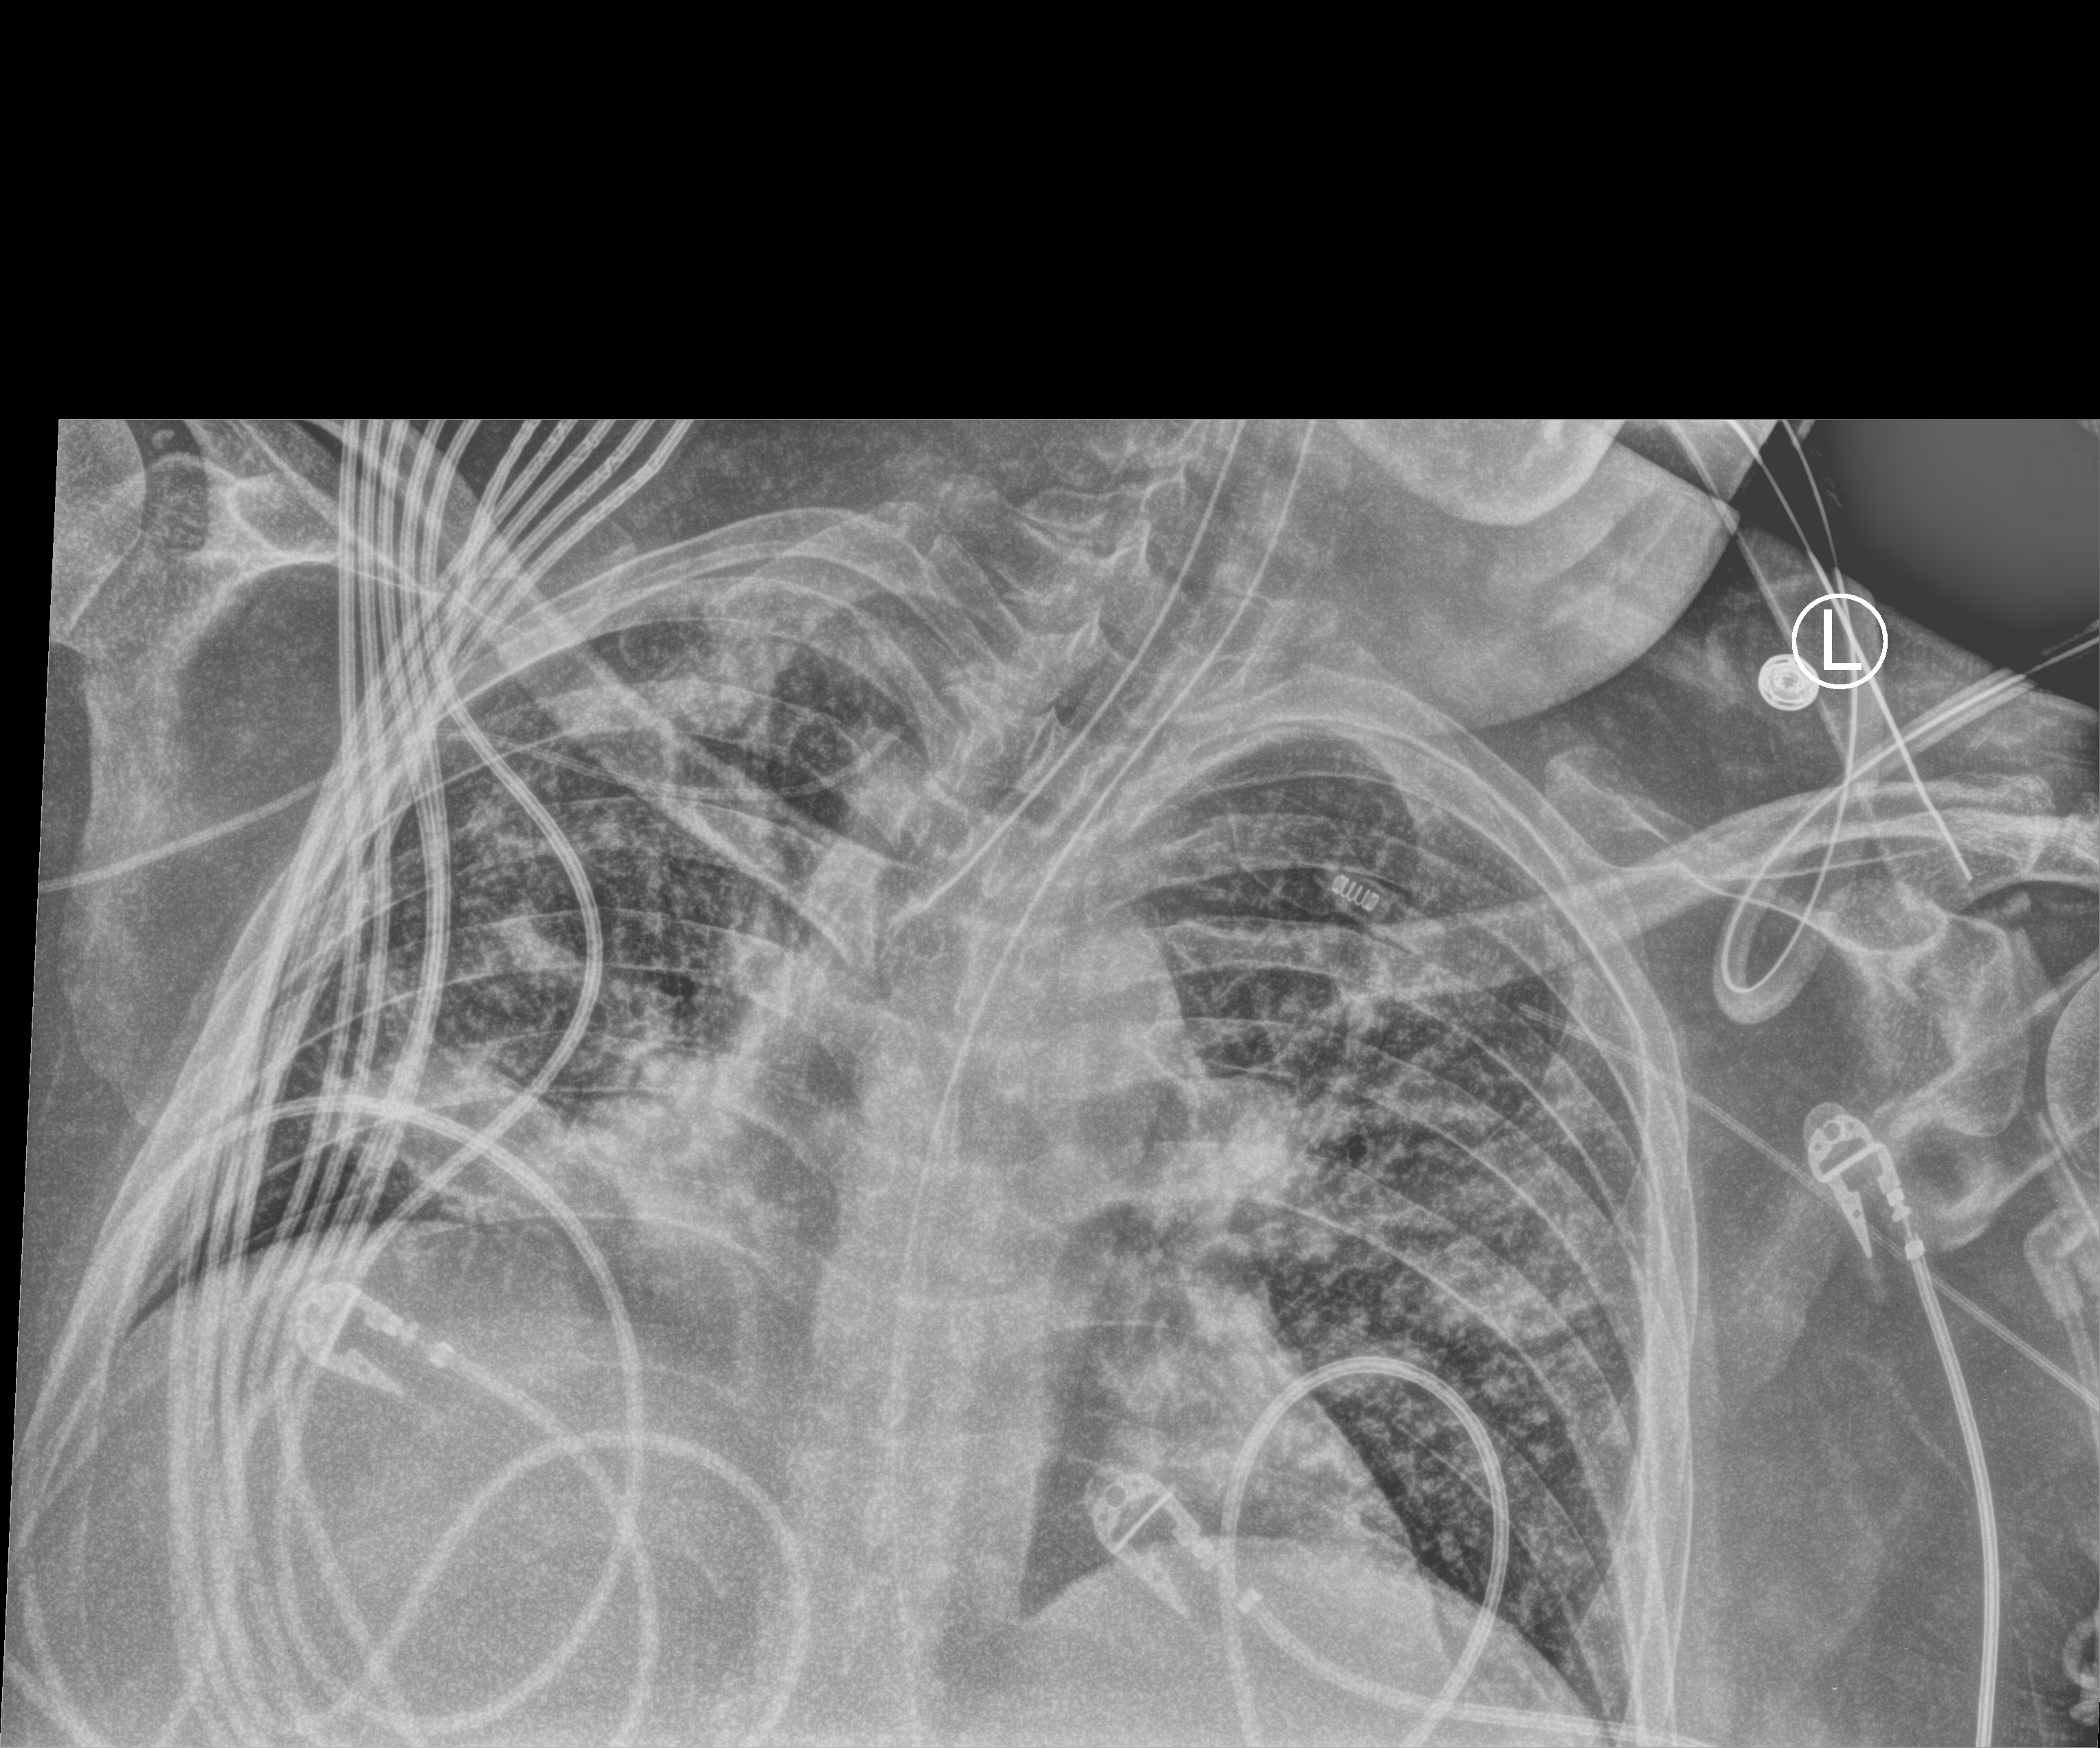
Chest X-ray (portable), anteroposterior (AP) projection. Patient hospitalised with COVID-19, aged 18–59 years.
Hospital-stay facts (about this admission, not read from this image; timing relative to this image not recorded): admitted to intensive care during this hospital stay: yes.